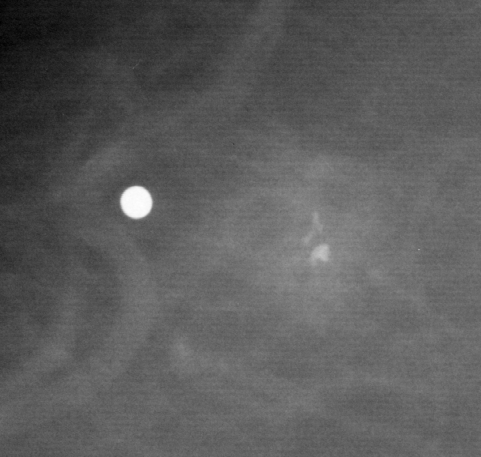
Crop from a digitized film mammogram around one marked abnormality; right breast; MLO view; BI-RADS breast density category 1 (scale 1–4).
Finding: calcifications, morphology fine linear branching, distribution clustered; BI-RADS assessment category 4; pathology (as recorded): benign.